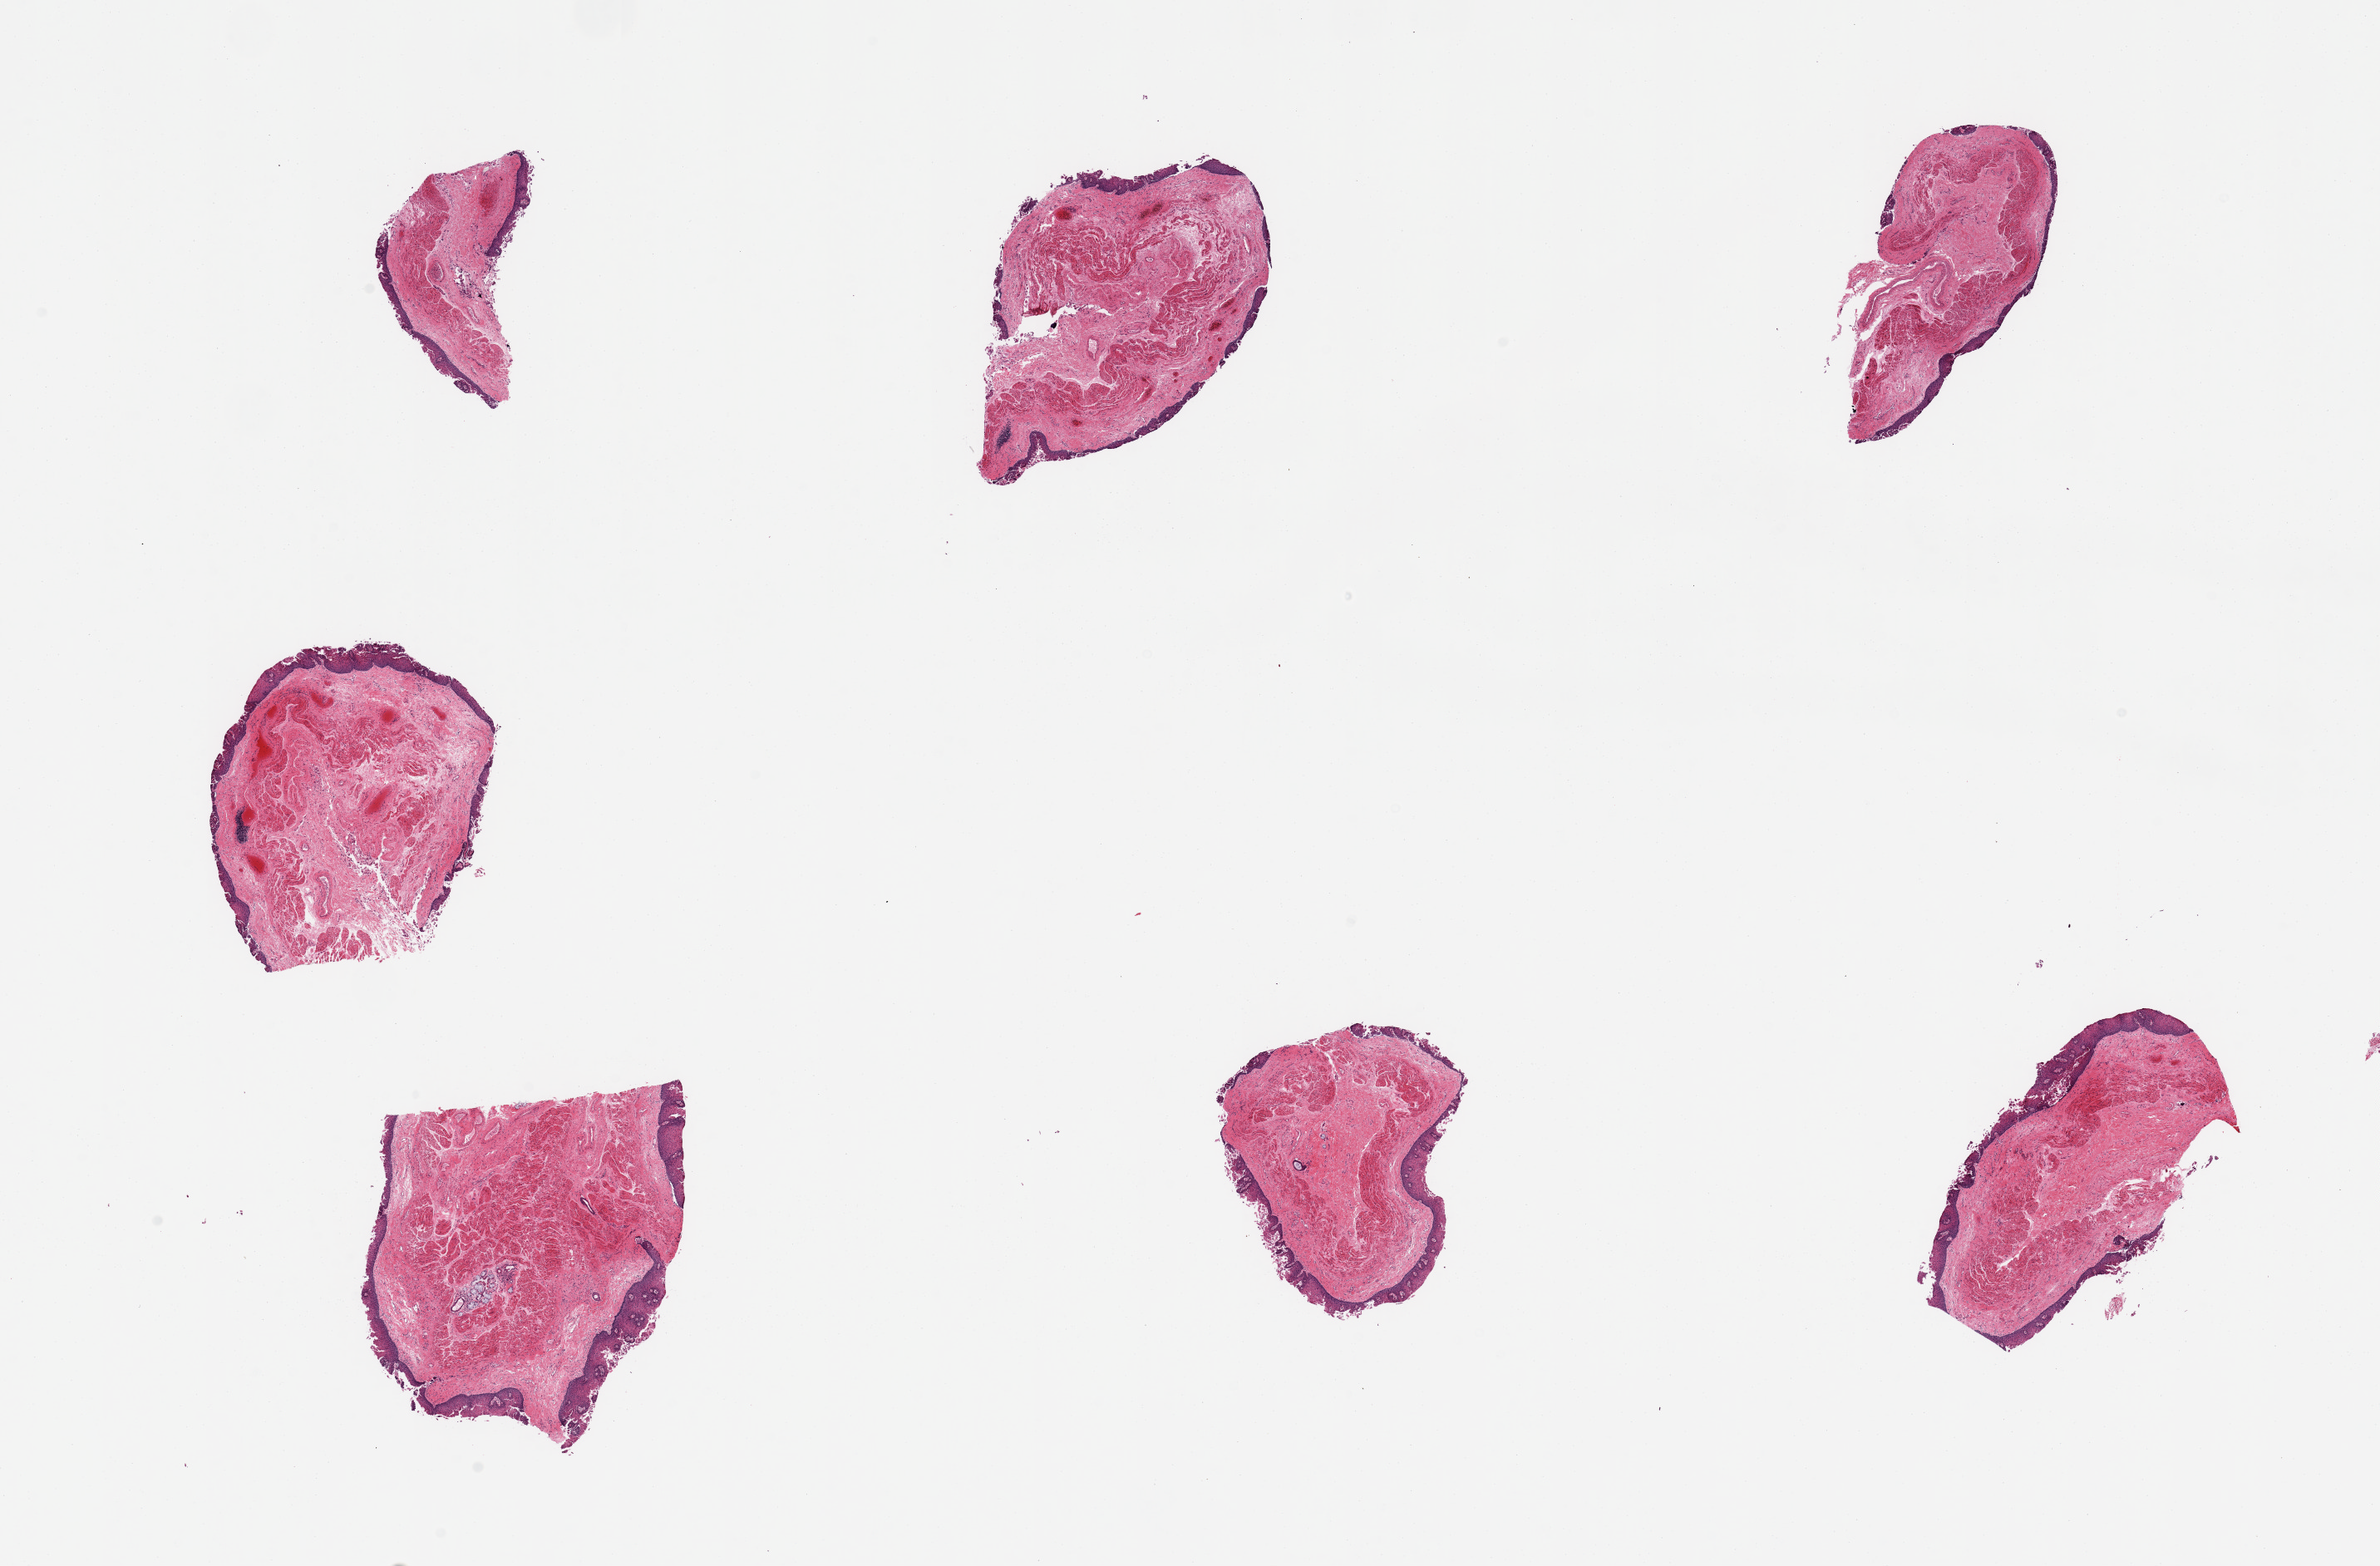
Whole-slide image, haematoxylin and eosin stain — low-resolution overview of the scanned area, about 22.6 x 14.9 mm. PAXgene-fixed, paraffin-embedded tissue. Target tissue: esophageal mucous membrane. Donor tissue sample. Male donor.
• reviewer comment on this tissue sample: 7 pieces; partially sloughed epithelium, remainder is well preserved